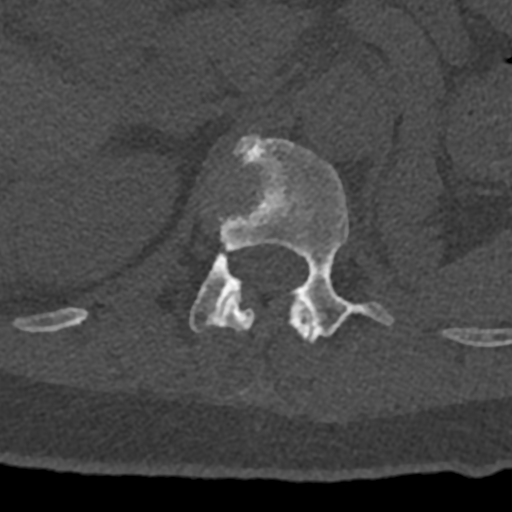
CT including the spine, one axial slice; slice 456 of 797 in the series (ordered by position); 120 kVp; bone window (W 1800 / L 400 HU); 0.5 mm slice thickness; 512 × 512 image matrix, field of view 160 × 160 mm. Male patient, age 74 years. Case-level facts recorded for this patient, not image findings: primary cancer: renal.
Annotated regions visible in this slice (semi-automatically segmented with operator editing):
- L1 vertebra: bounding box (x1, y1, x2, y2) in pixels: (190, 134, 394, 342)
- T12 vertebra: (70, 298, 313, 343)